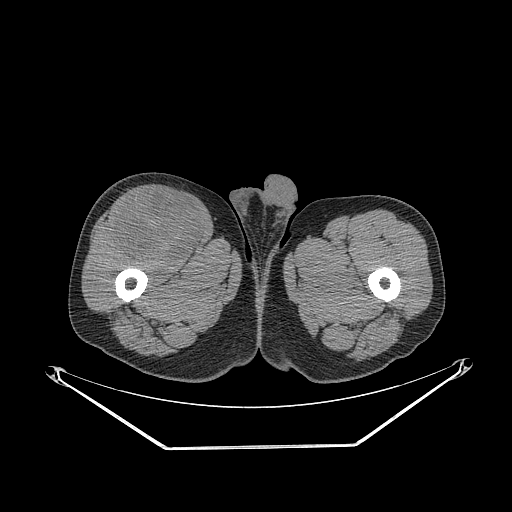
CT of an extremity soft-tissue mass (from a PET/CT study), one axial slice. Slice 286 of 311 in the series (ordered by position). Reconstruction kernel STANDARD. 140 kVp. Soft-tissue window (W 400 / L 40 HU). 512 × 512 image matrix, field of view 500 × 500 mm. Male patient. Case-level facts recorded for this patient, not image findings: histological type: pleiomorphic leiomyosarcoma; grade: intermediate; site of the primary tumour: right thigh.
Outlined on this slice (expert contour drawn on MRI and transferred to this co-registered scan by the dataset authors):
- gross tumour volume including surrounding oedema: bounding box <112,192,204,261> (left, top, right, bottom; pixels)
- gross tumour volume (mass): <112,192,204,261>